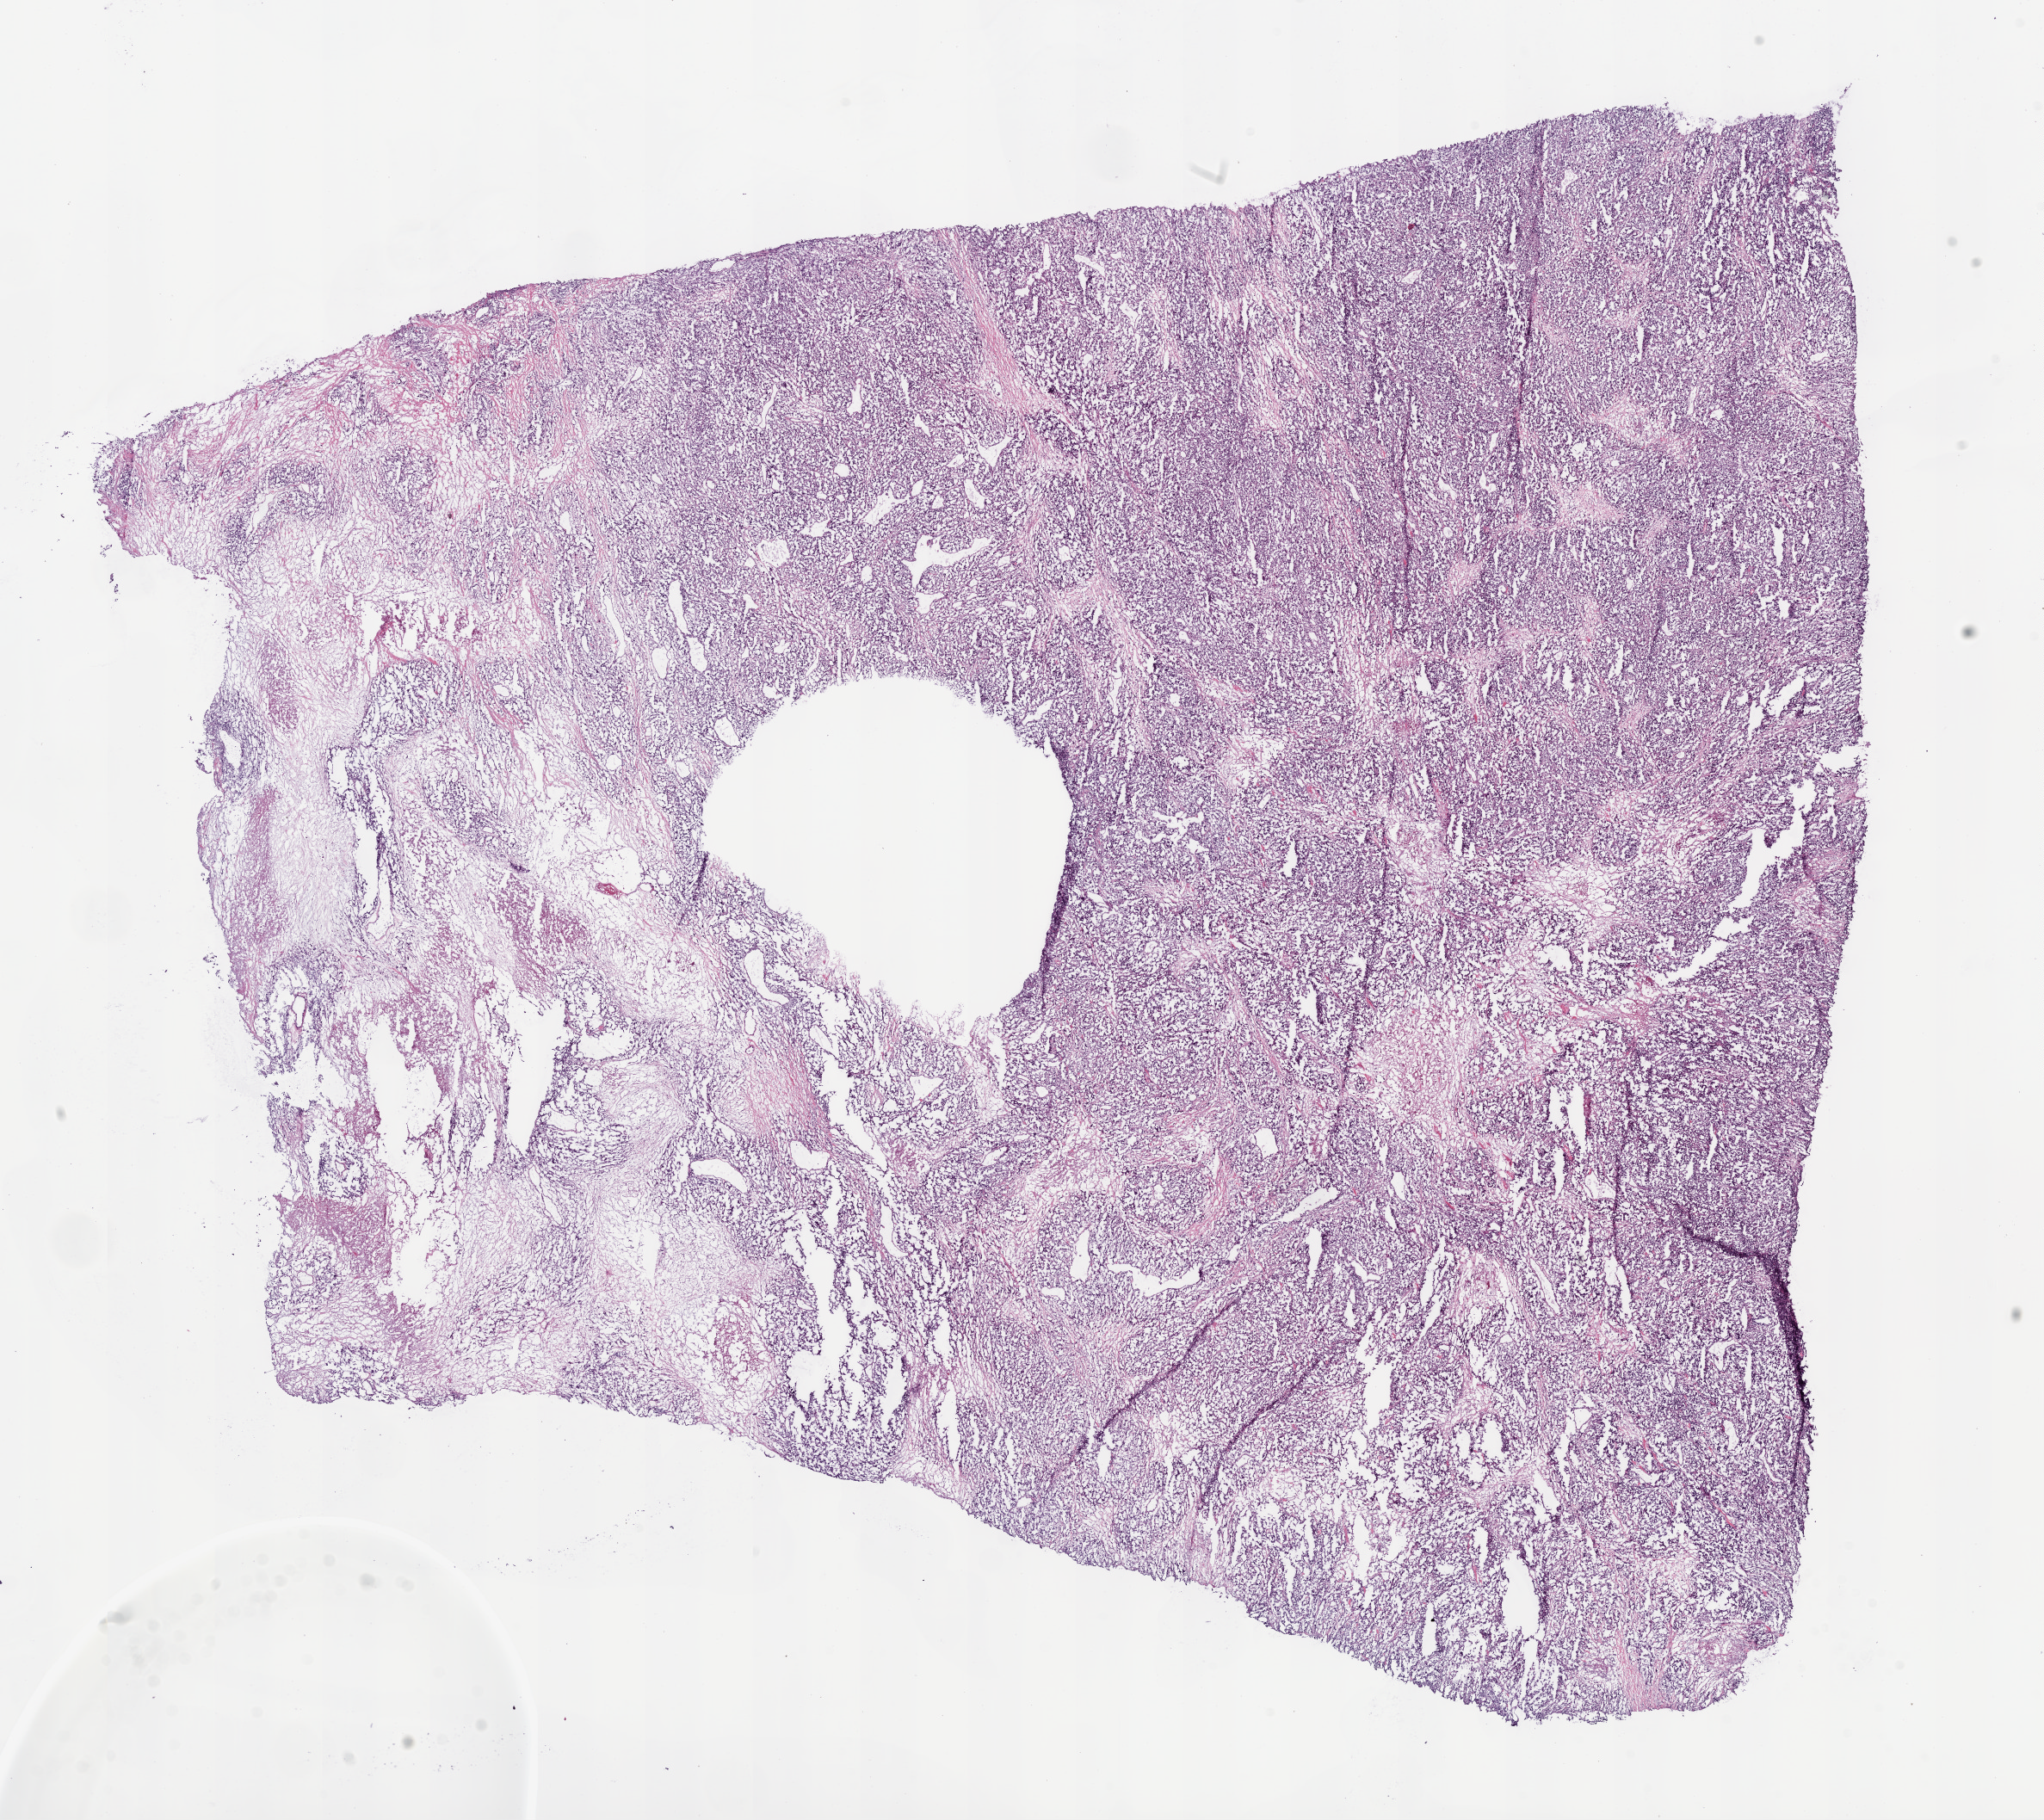
Digitized Hematoxylin and eosin (H&E) stained tissue section (whole slide), whole scanned area (about 19.1 x 17.0 mm) shown as a low-resolution overview; frozen section from the bottom of the tissue portion; kidney, primary tumour sample. Female, age 74 years at initial diagnosis. Histologic grade: G4 (undifferentiated). Pathologist review of this section (percent, as recorded): tumour cells 84%, tumour nuclei 80%, normal cells 0%, stromal cells 15%, necrosis 1%.
* laterality: right
* AJCC pathologic stage: IV
* histologic diagnosis: Clear cell adenocarcinoma, NOS
* lymph nodes positive (case pathology): 0 of 10 examined